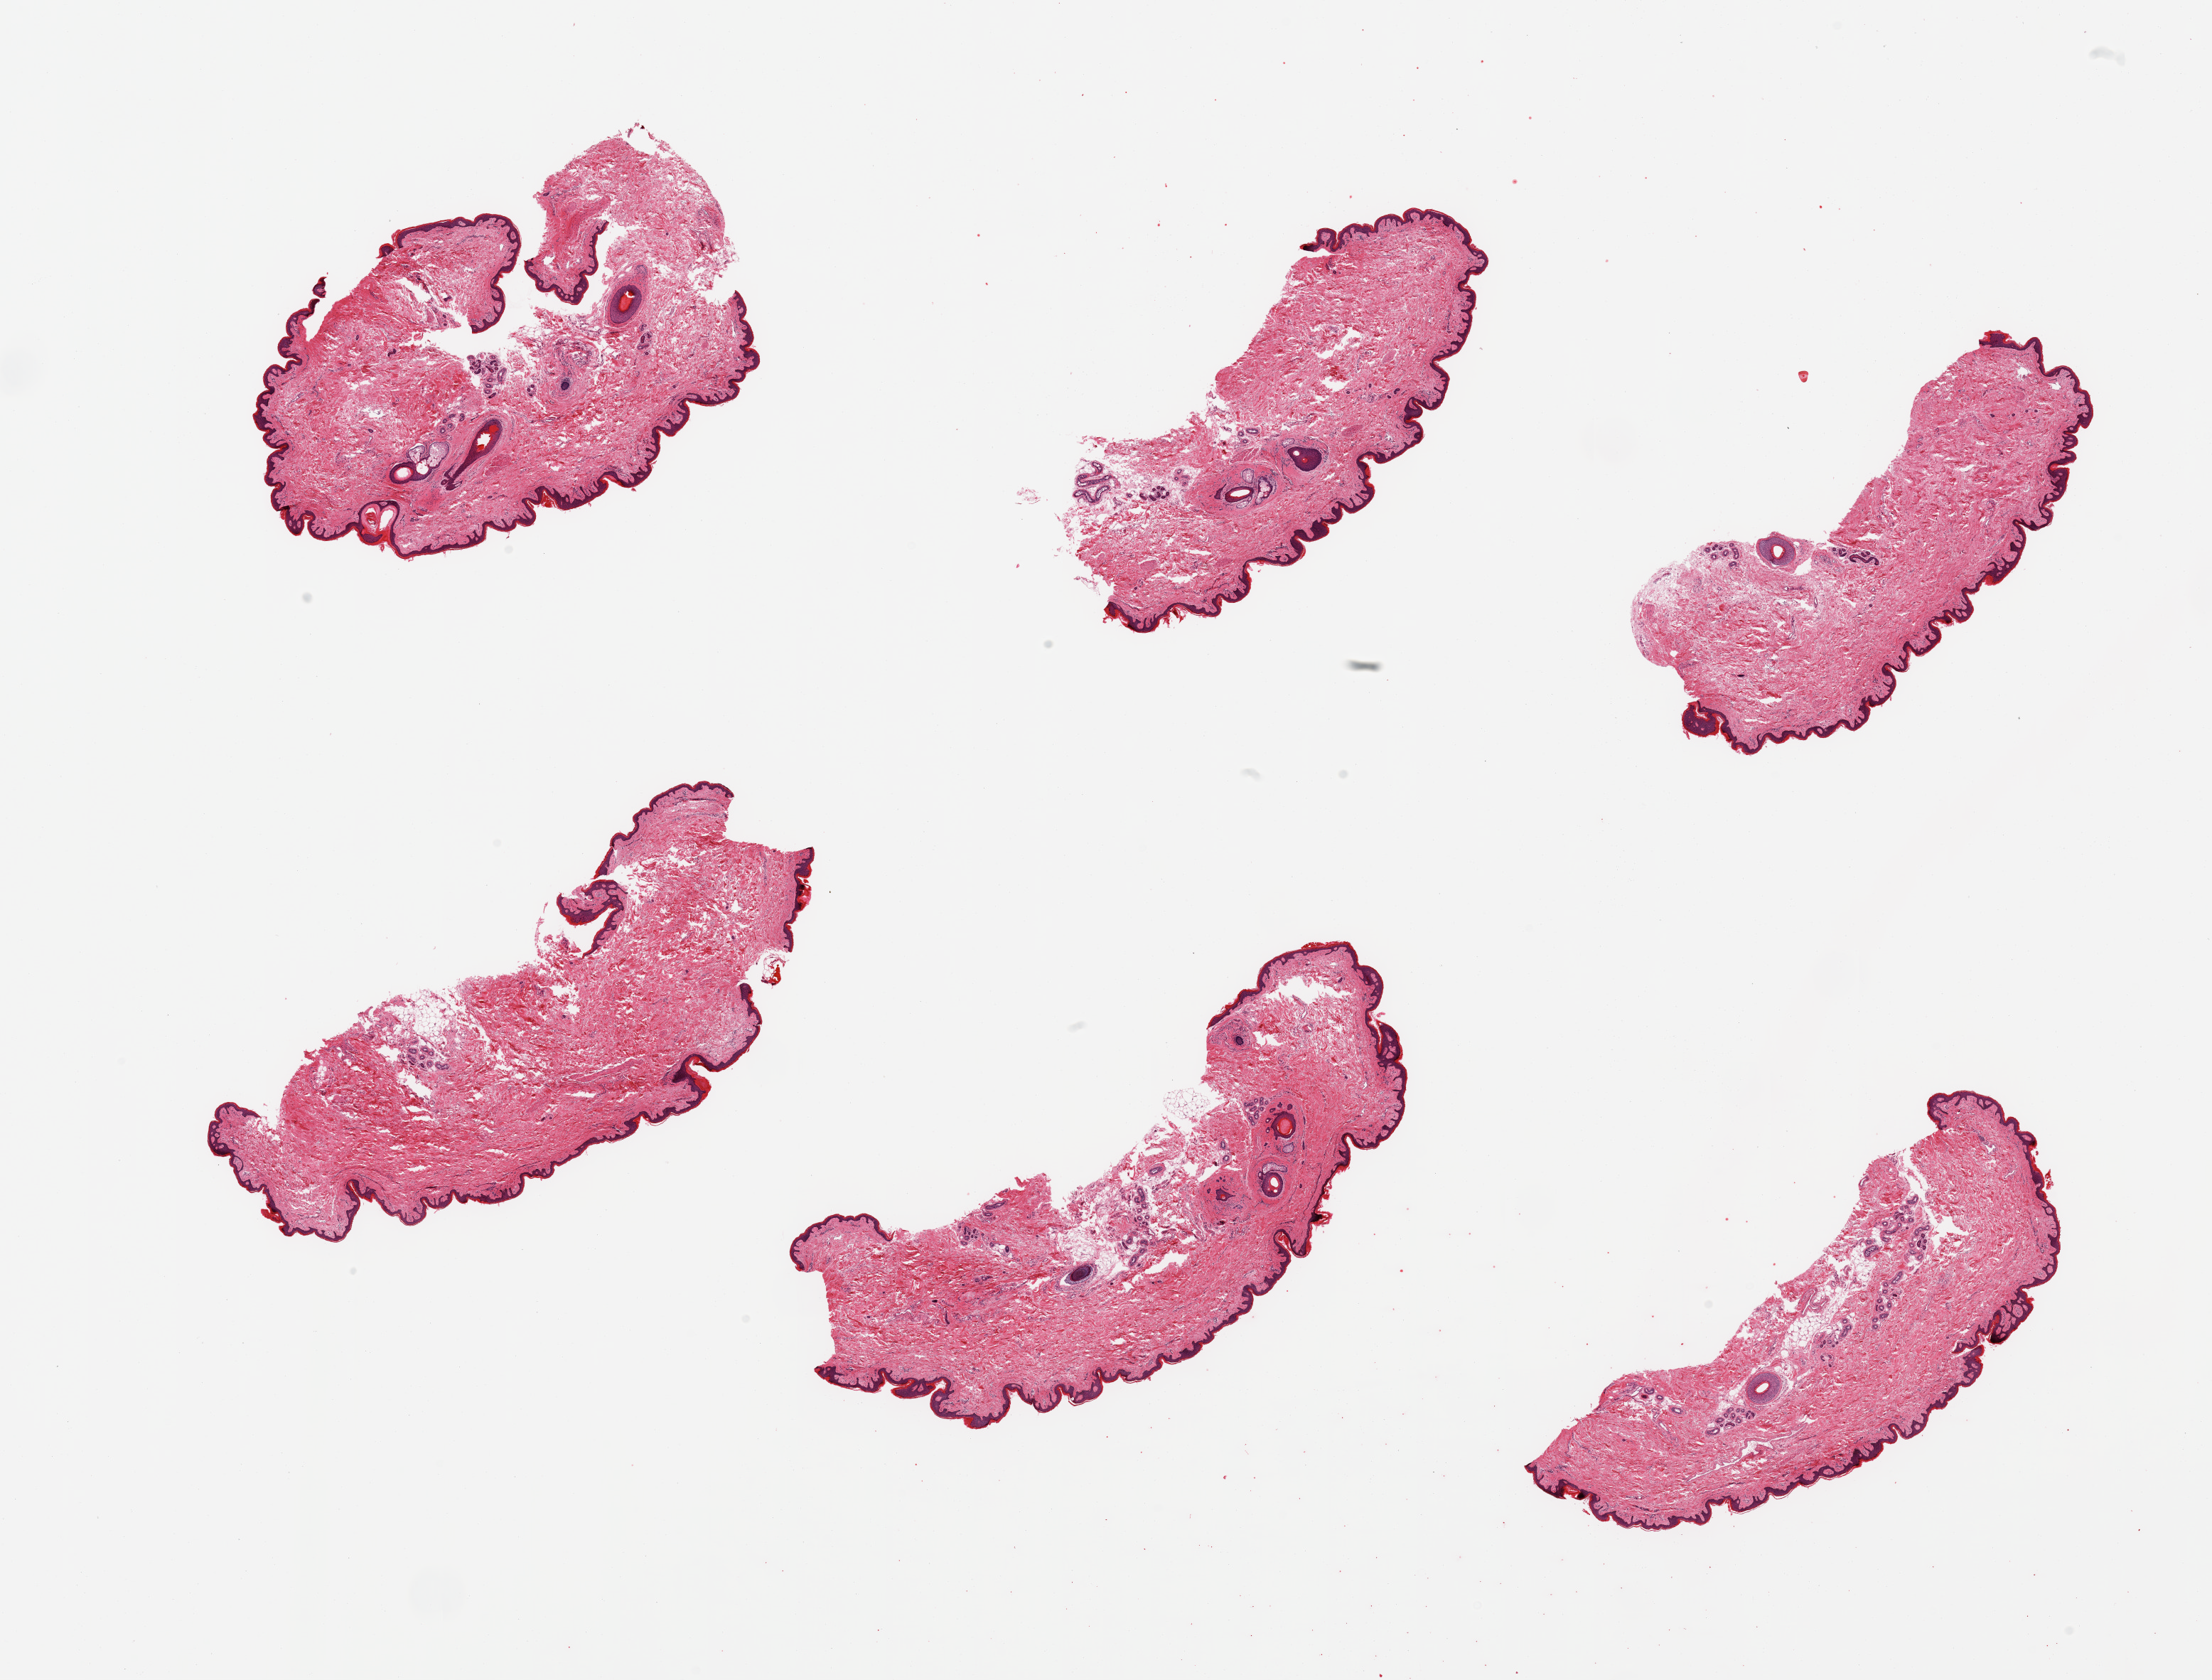
H&E whole-slide image — a low-resolution overview of the entire scanned area, about 24.6 x 18.7 mm, PAXgene-fixed paraffin-embedded (PFPE) section, section of skin of suprapubic region (target tissue), tissue donor sample. Male donor.
Reviewer comment on this tissue sample: 6 pieces; well trimmed; 5% dermal fat.